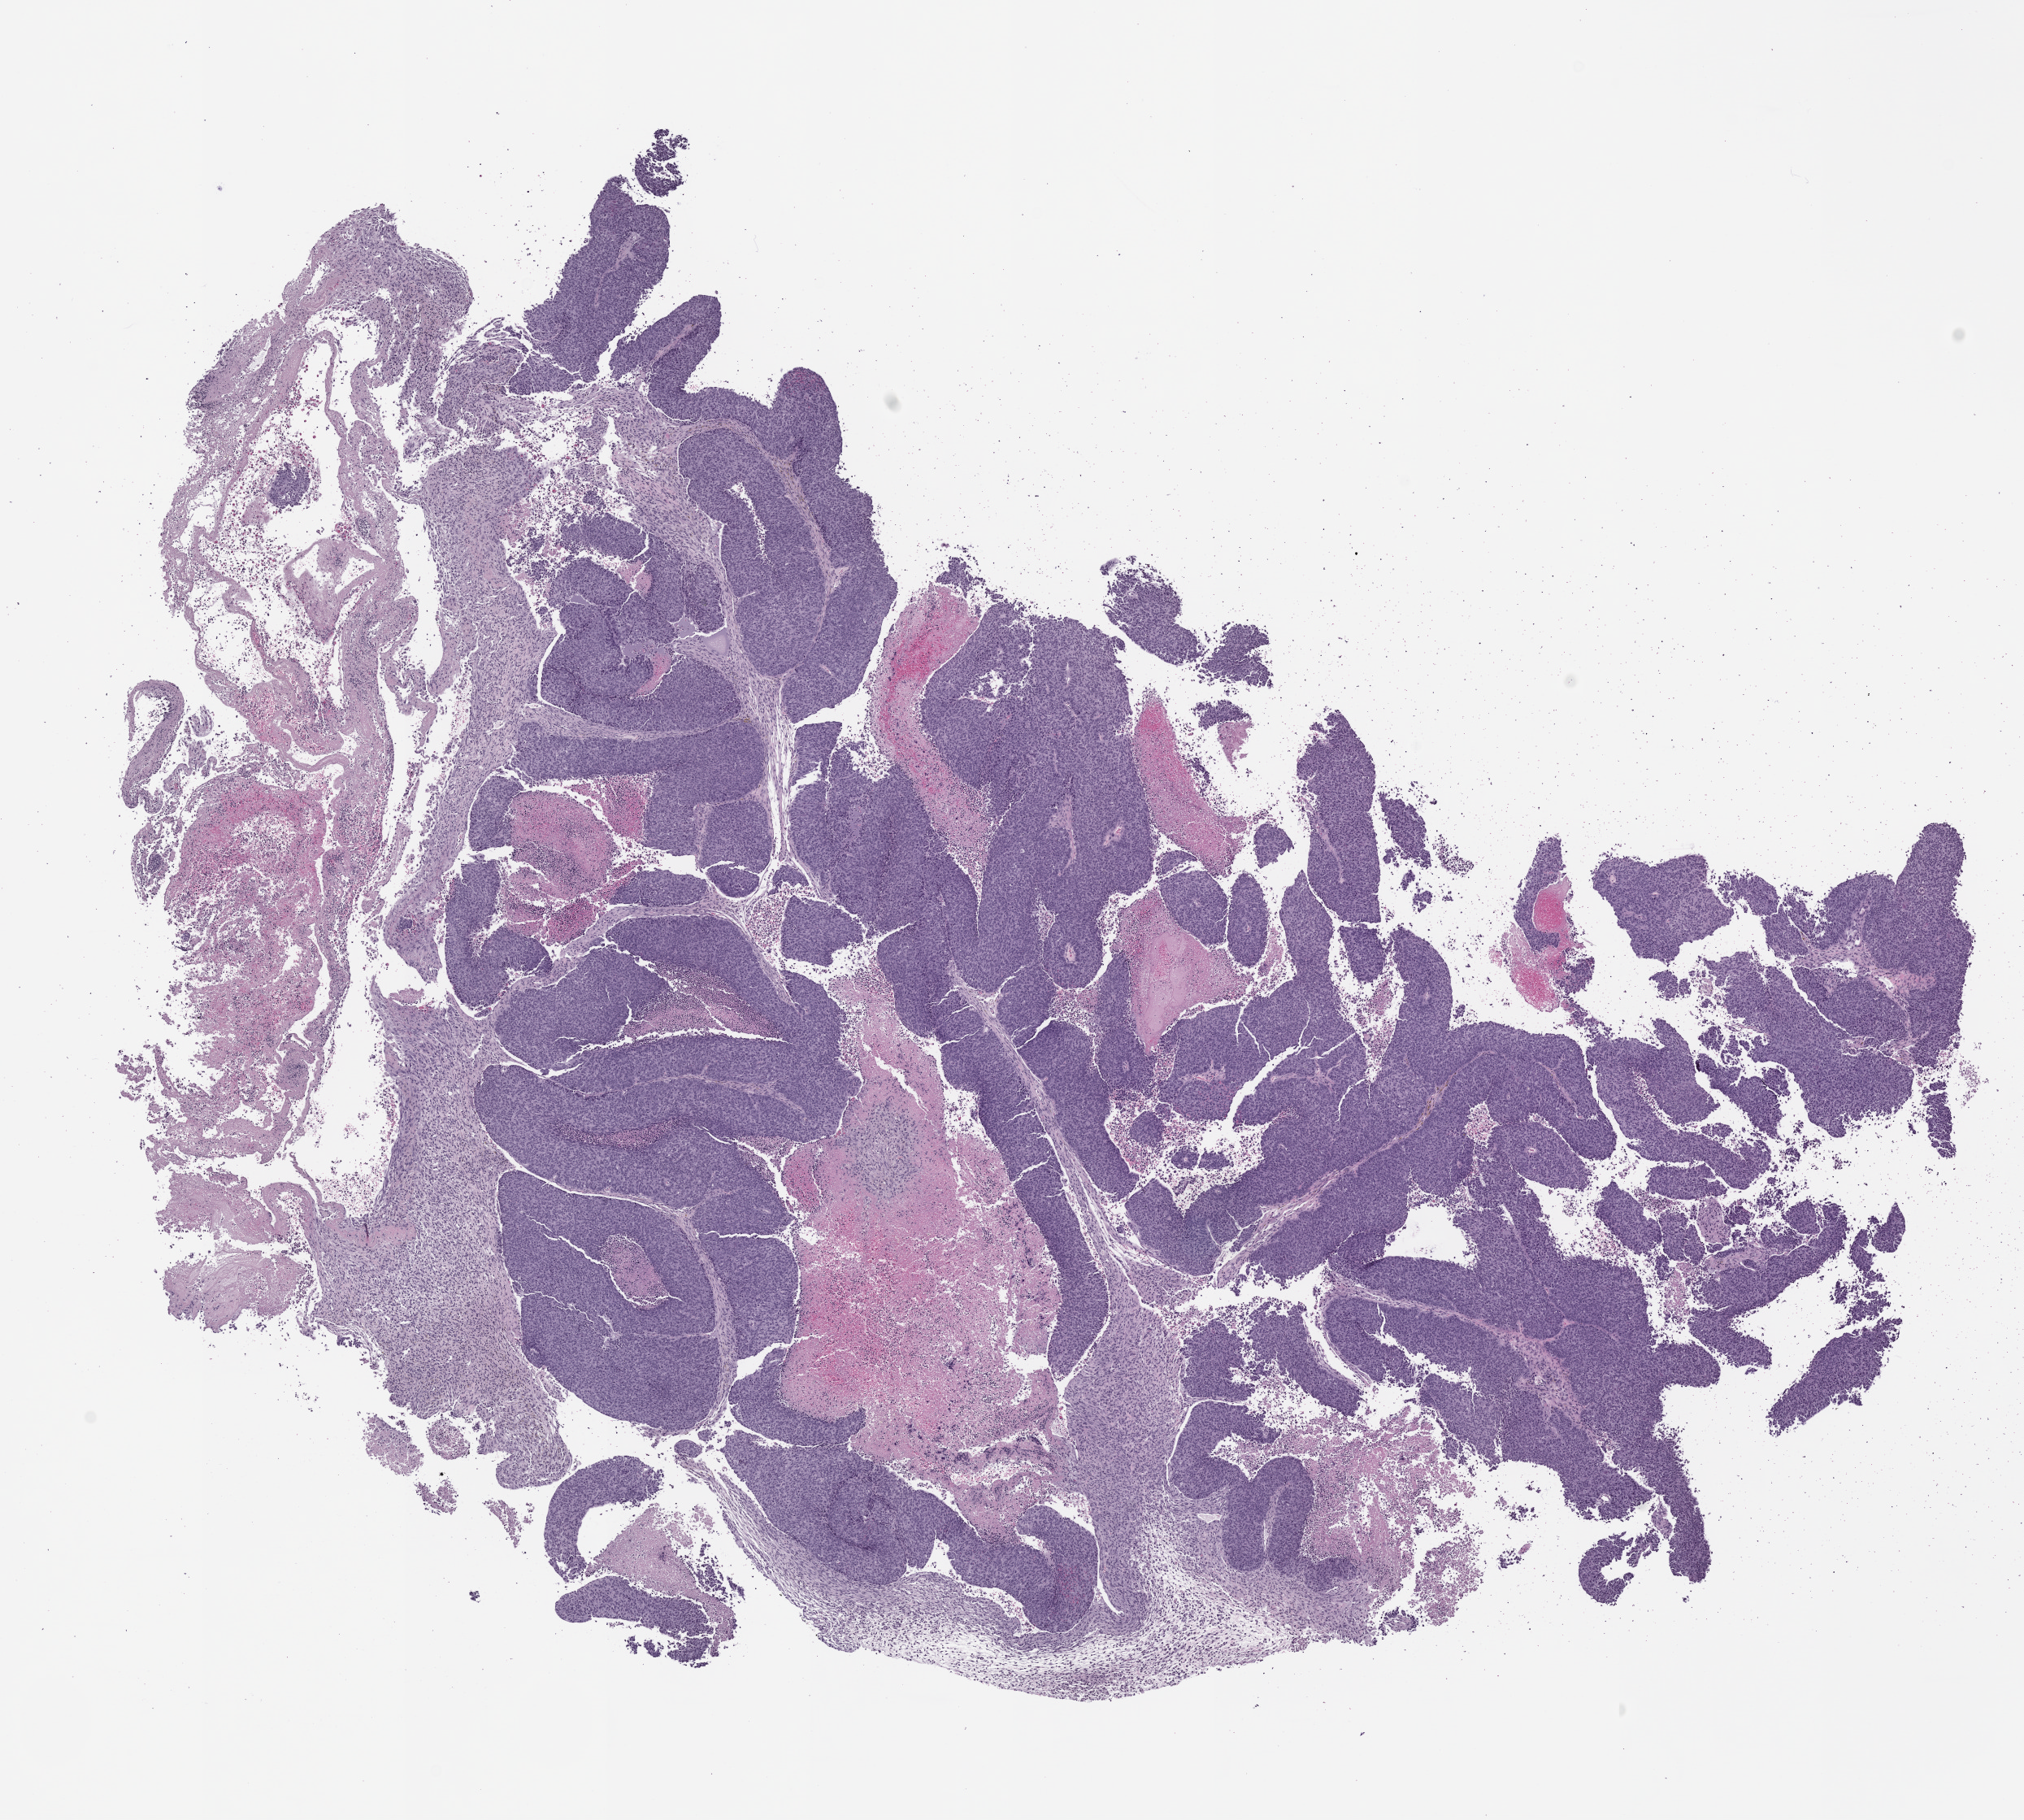
Whole-slide image, H&E: patient-derived xenograft (human tumor grown in a mouse), passage 1 — shown as a low-resolution overview of the whole scanned area (about 10.0 x 9.0 mm), FFPE section, tumor site category: vagina.
Originating patient diagnosis: Vaginal Carcinoma.